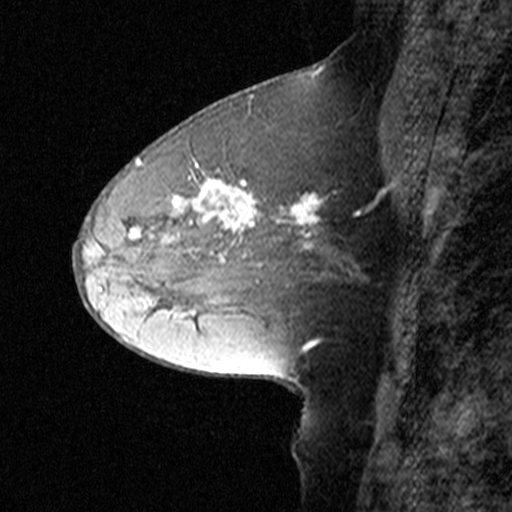
Breast MRI (dynamic contrast-enhanced), one sagittal slice; slice 21 of 44 in the series (ordered by position); dynamic contrast-enhanced study with each time point stored as its own series, time point 2 of 3 at this slice position (early post-contrast, ordered by acquisition time); 1.5 T; TE 4.5 ms, TR 11 ms; 3 mm slice thickness; 512 × 512 image matrix, field of view 200 × 200 mm. Patient: female, 50 years. From the clinical record (not read from this slice): setting: breast cancer imaged before/during neoadjuvant chemotherapy; receptor status: HR-positive, HER2-negative.
Annotated regions visible in this slice (semi-automatically segmented with operator editing):
- analysis volume of interest (the breast-tissue region the enhancement analysis was run in; not a lesion): bounding box <126,162,329,291> (left, top, right, bottom; pixels)
- tumour enhancement mask (voxels above the 90 % enhancement threshold inside the analysis volume of interest): <131,162,326,262>